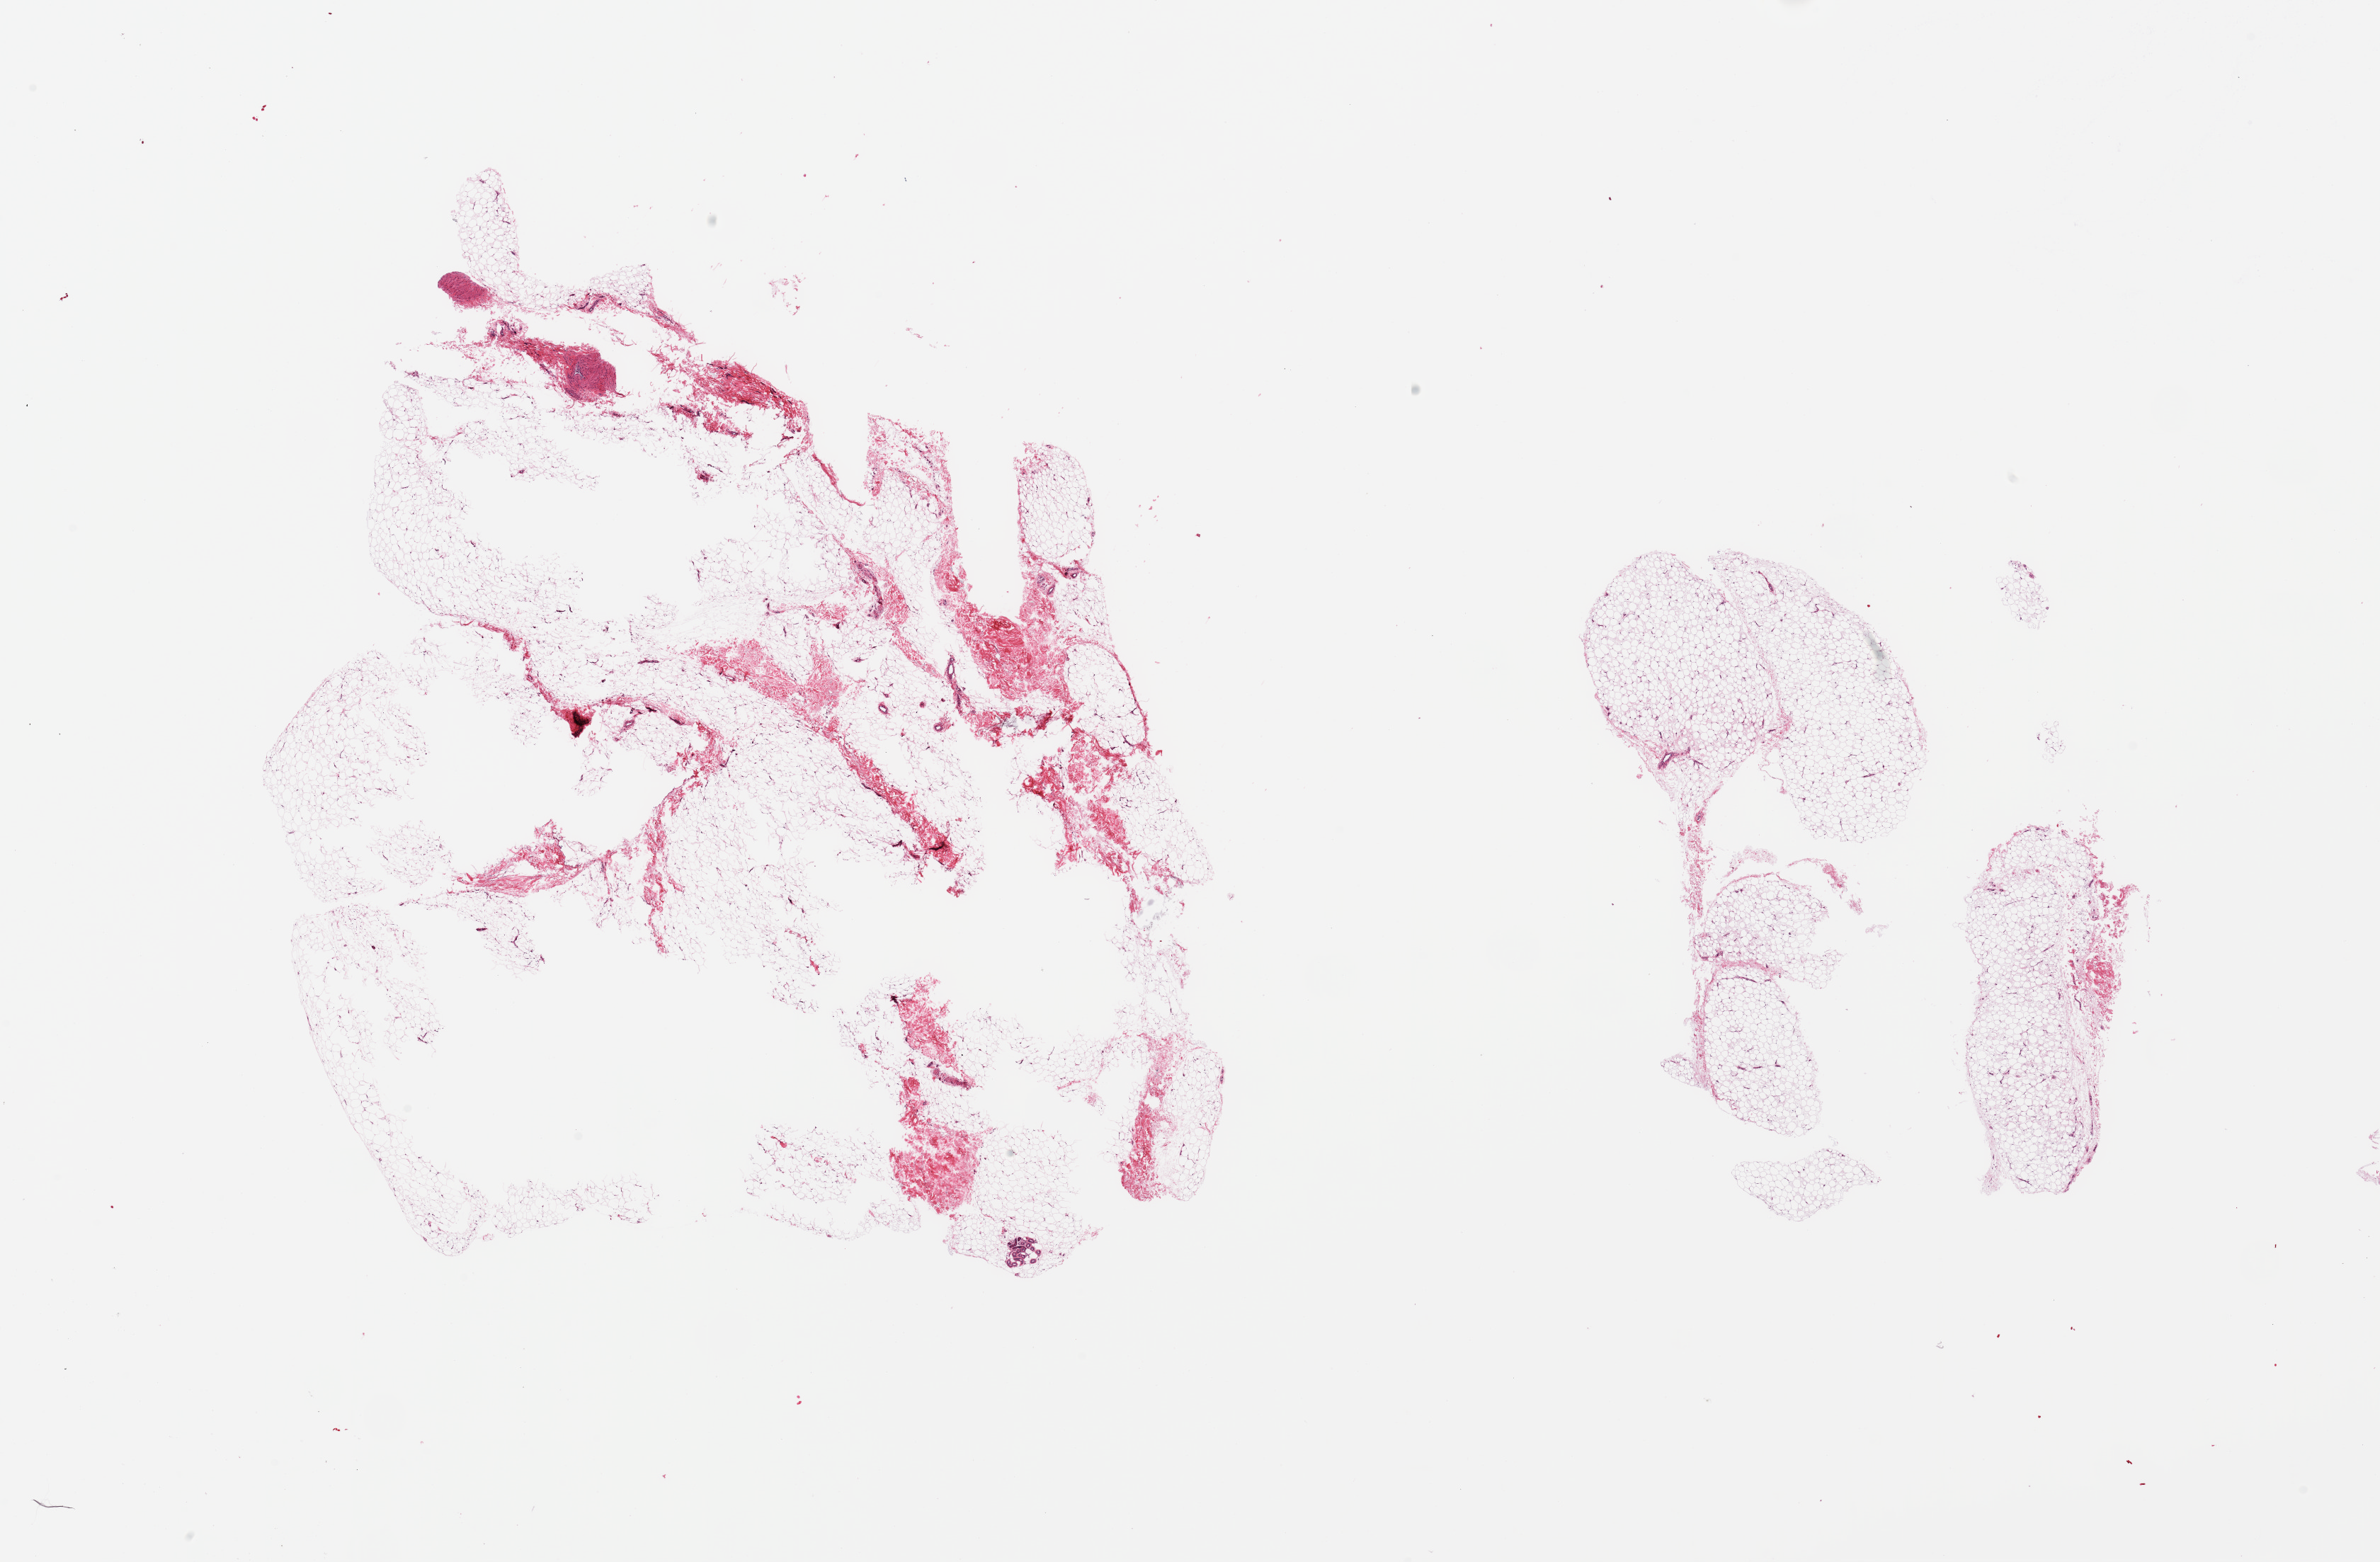
Digitized haematoxylin and eosin-stained section, brightfield — whole scanned area (about 26.6 x 17.4 mm) shown as a low-resolution overview; PAXgene-fixed, paraffin-embedded tissue; sampled site (target tissue): adipose tissue; tissue donor sample. Male donor.
* reviewer comment on this tissue sample: 2 pieces, fascia/vascular elements ~5-10% of tissue